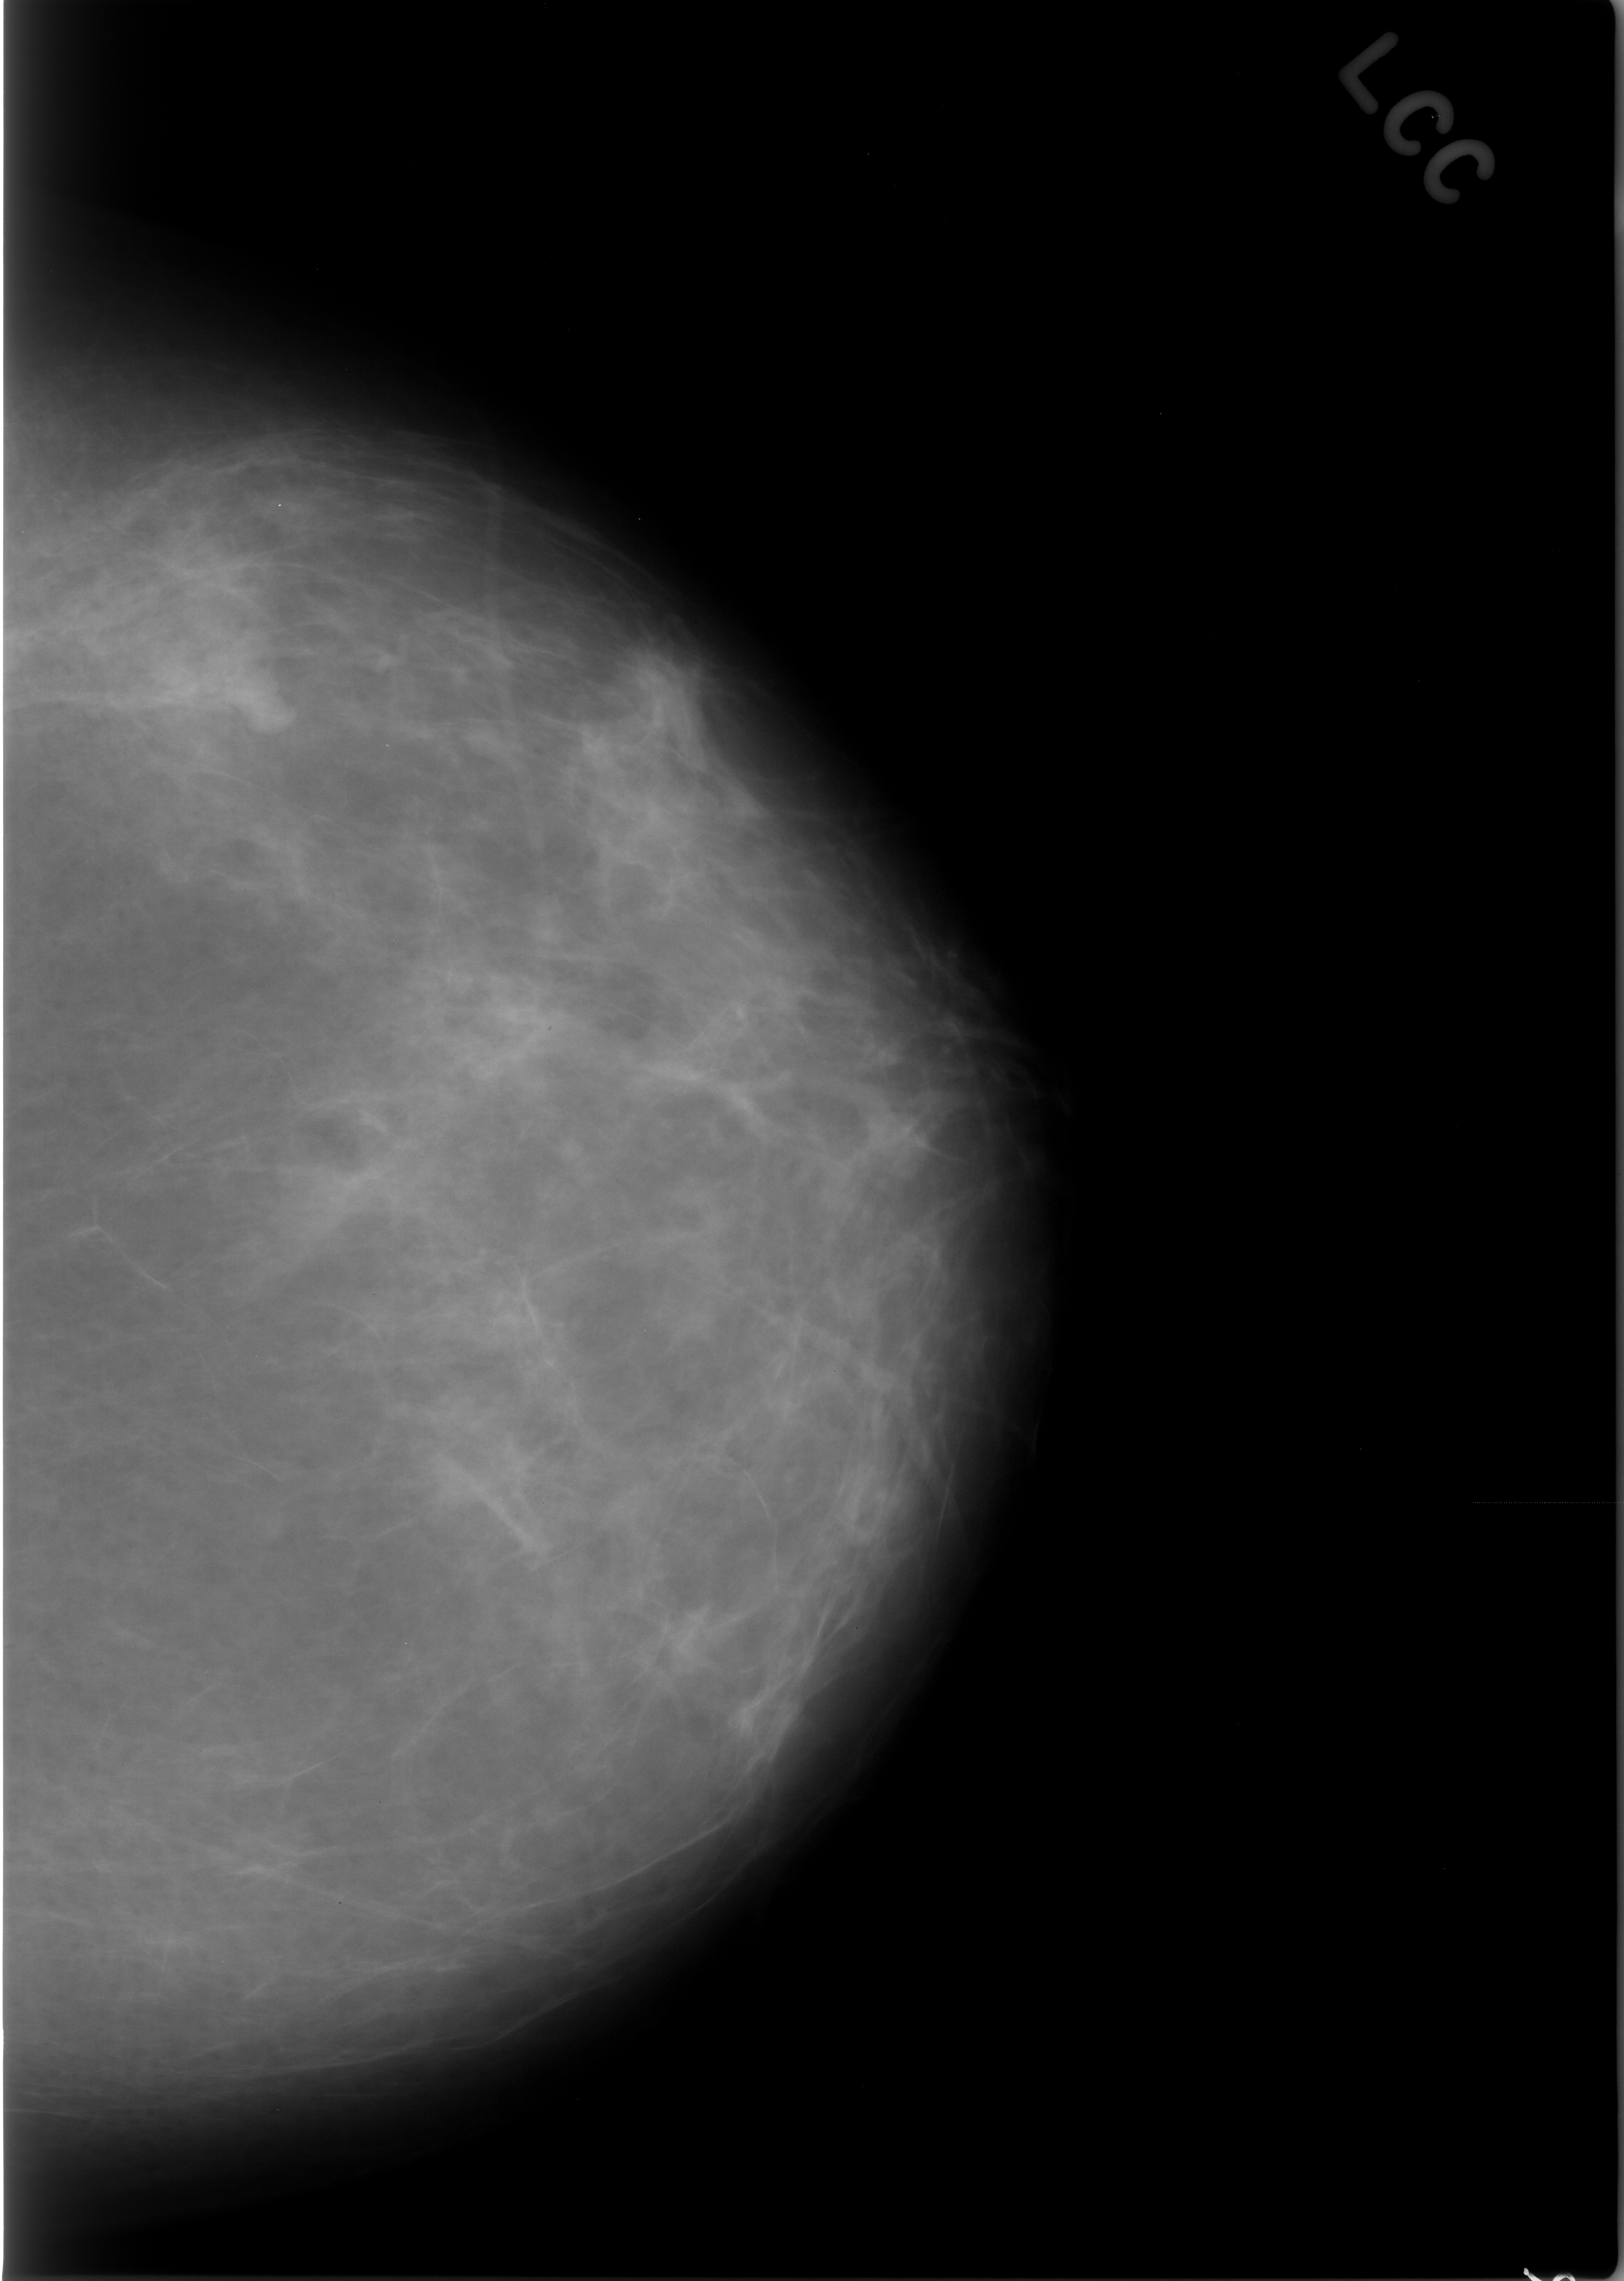
Mammogram (digitized film), left breast, CC view, BI-RADS breast density category 1 (scale 1–4).
Abnormality record for this image: mass, shape irregular, margins spiculated; BI-RADS assessment category 4; benign; no additional work-up was recommended (benign without callback).